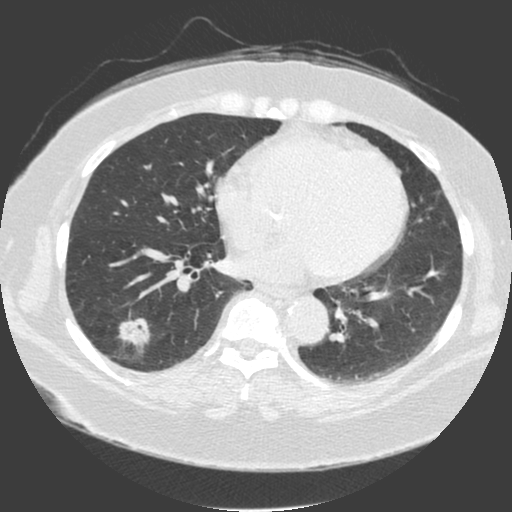
Chest CT (low-dose screening protocol), one axial image; third annual screen; lung window (W 1500 / L -600 HU); standard (soft-tissue) reconstruction kernel (C). Female participant, aged 56 years at enrolment.
Lesion marked by an expert reader, bounding box (x1, y1, x2, y2) in pixels: (107, 305, 158, 353). The screening reader recorded 4 non-calcified nodules or masses ≥4 mm on this exam (left lower lobe, right lower lobe, right lower lobe, right lower lobe); which of them this box marks is not recorded. Later outcome: lung cancer diagnosed 20 days after this screen — adenosquamous carcinoma, right lower lobe, poorly differentiated (G3), stage IA (AJCC 6th edition), 25 mm at pathology.